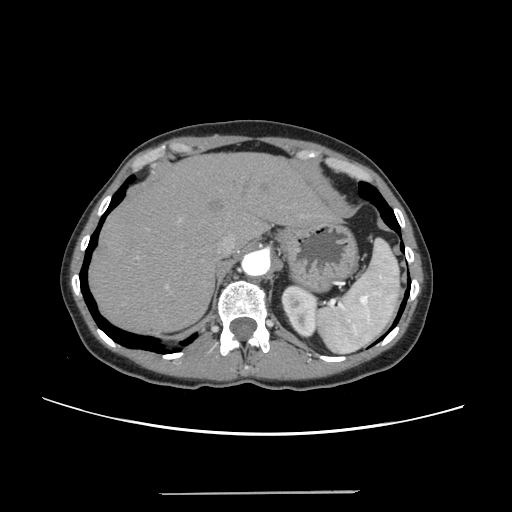
Contrast-enhanced abdominal CT, one axial slice; position 191 of 240 along the scan axis; intravenous contrast given; soft-tissue window (W 400 / L 40 HU); 512 × 512 image matrix, field of view 371 × 371 mm. Female patient, age 60 years. From the clinical record (not read from this slice): diagnosis: colorectal cancer liver metastases, imaged before liver resection; multiple liver metastases: no; largest metastasis: 1.5 cm; chemotherapy before resection: yes.
Annotated regions visible in this slice (expert manual segmentation):
- hepatic veins: box from (x=217, y=237) to (x=235, y=254) px
- liver: (x=90, y=154)–(x=332, y=333)
- planned liver remnant (the part of the liver to remain after resection): (x=90, y=154)–(x=332, y=333)
- portal vein (with intrahepatic branches): (x=166, y=217)–(x=181, y=288)